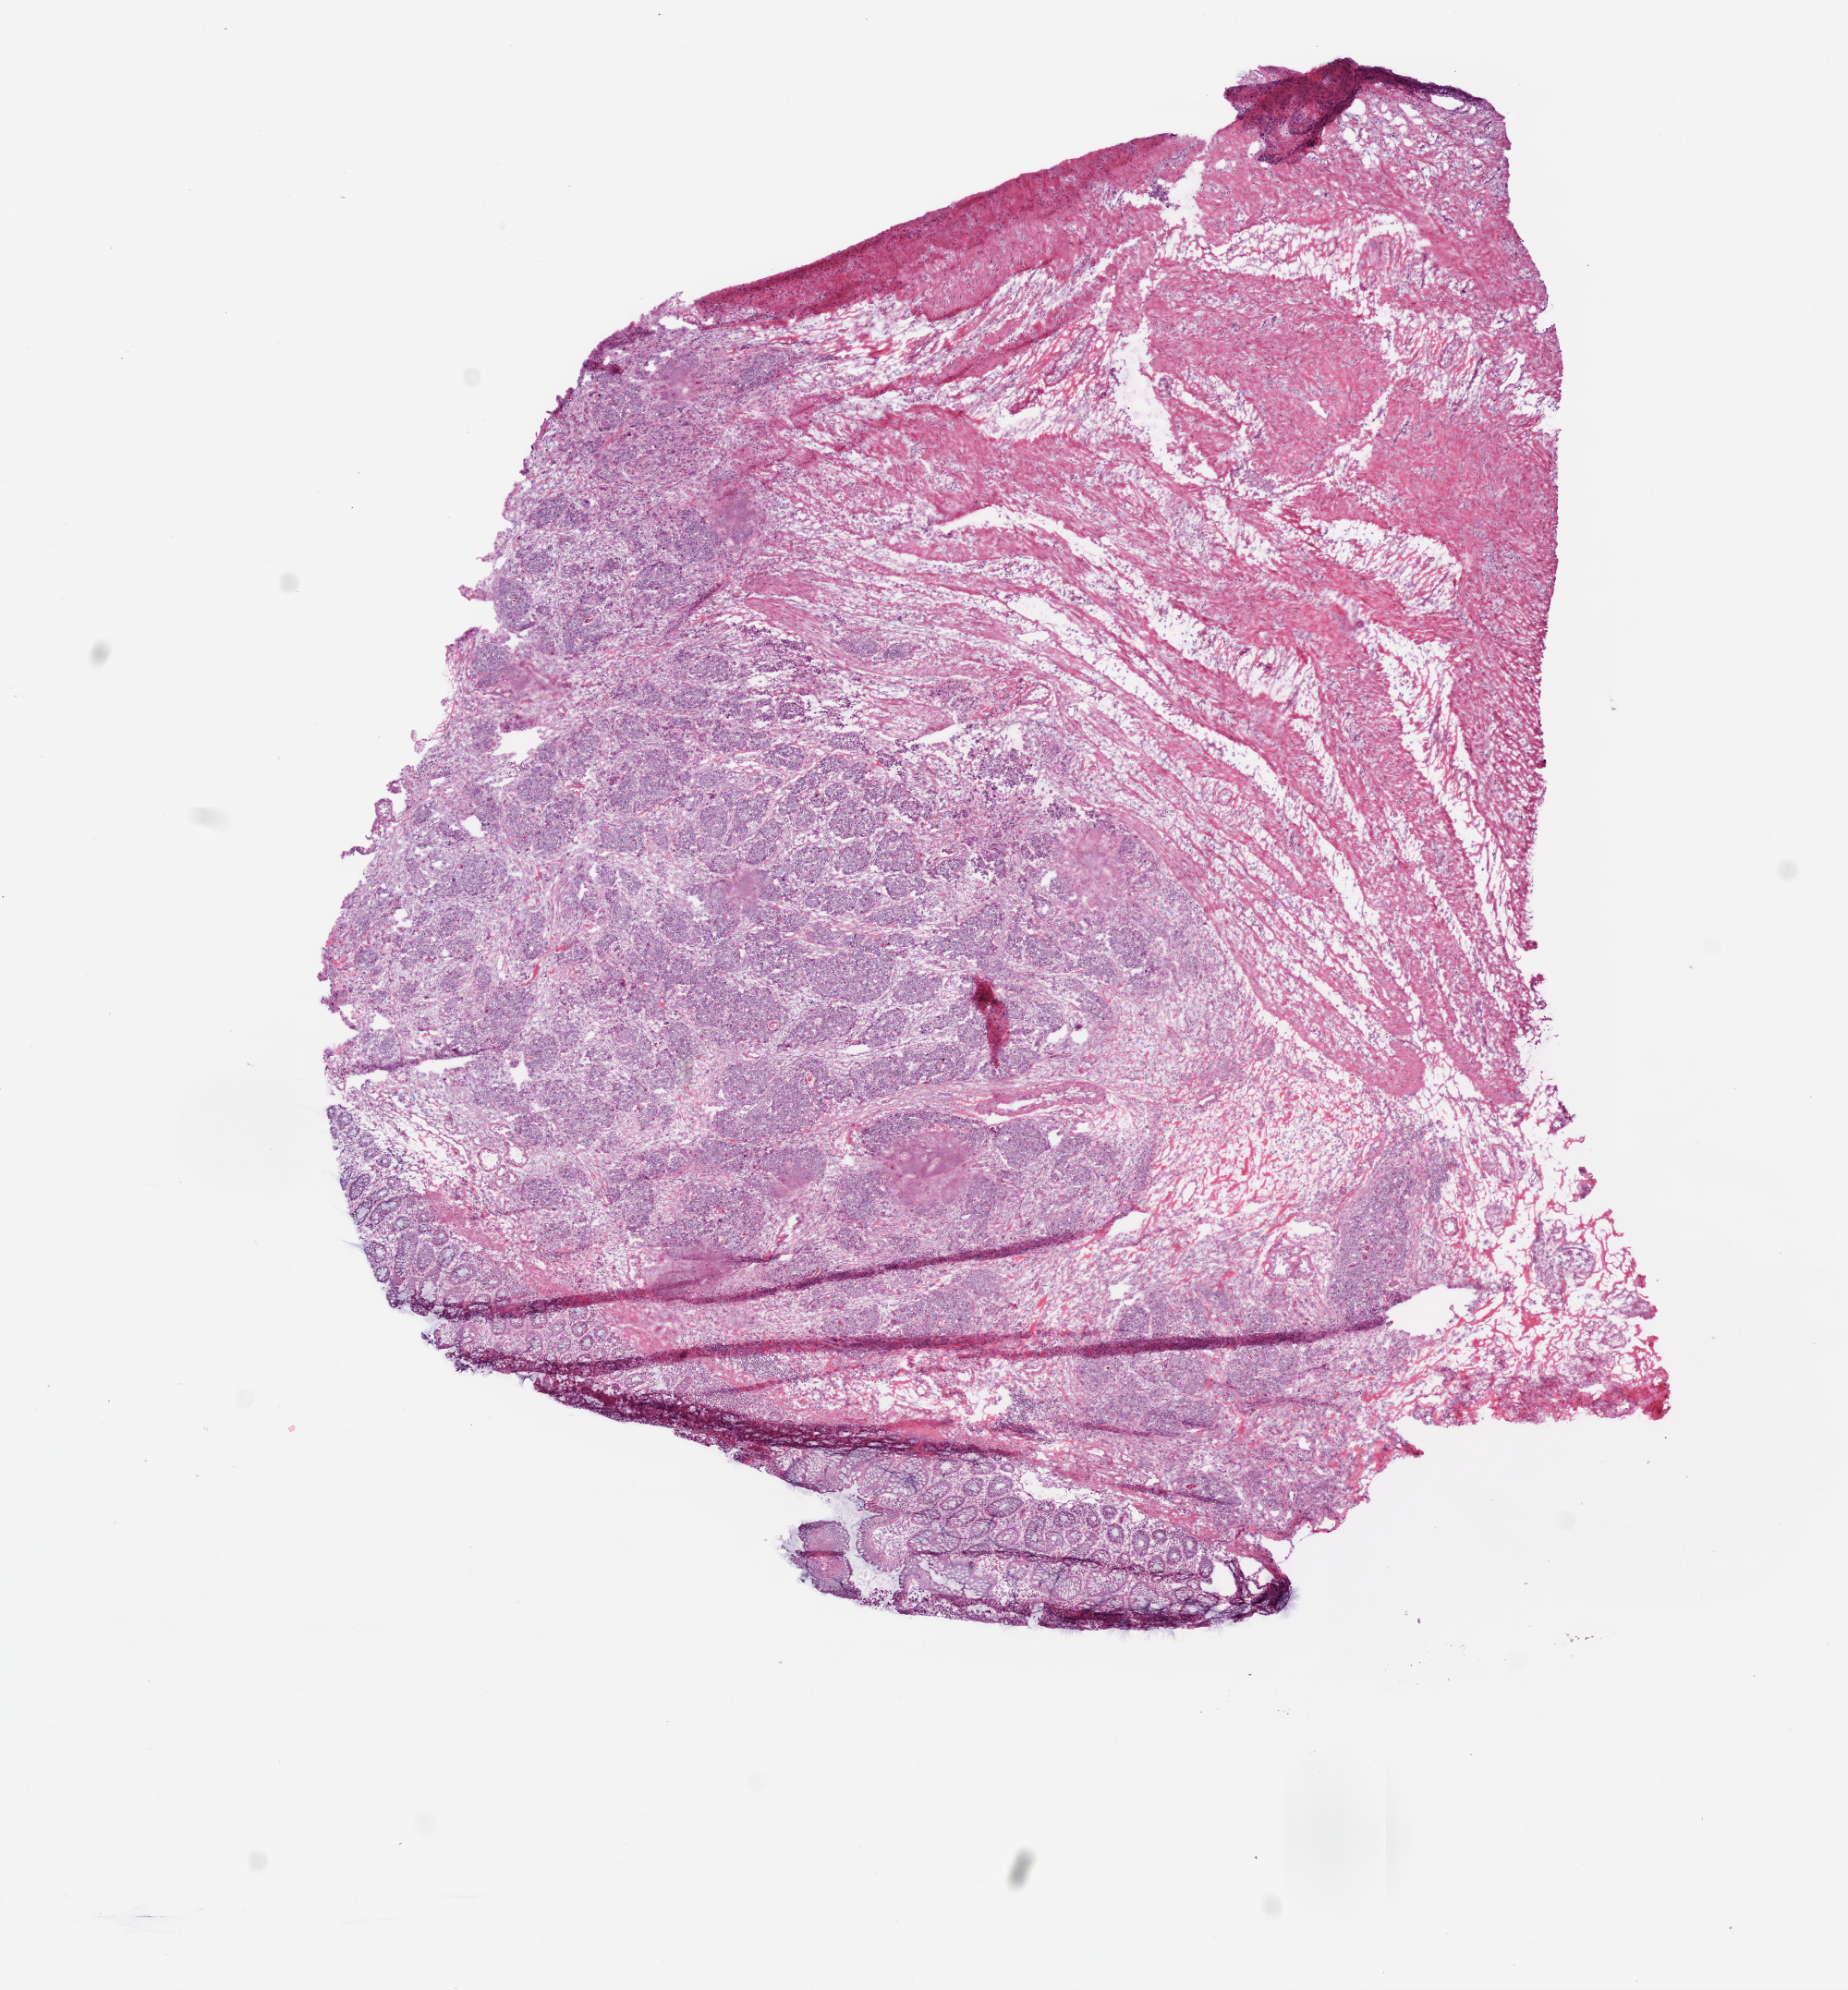
Digitized Hematoxylin and eosin (H&E) stained tissue section (whole slide) — a low-resolution overview of the entire scanned area, about 8.0 x 8.6 mm (slide scanned at 20x). Frozen section from the top of the tissue portion. Primary tumour sample from the colon. Male patient; age at initial diagnosis 73 years. Slide review estimates, as recorded: tumour cells 65%, tumour nuclei 75%, normal cells 30%, stromal cells 10%, necrosis 5%.
AJCC pathologic stage: IV (6th edition). Diagnosis: Adenocarcinoma, NOS (sigmoid colon).